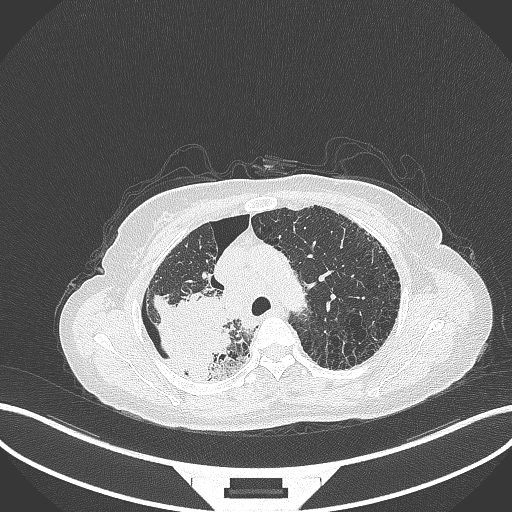
Chest CT, one axial slice. Reconstruction kernel B70f. 120 kVp. Lung window (W 1500 / L -600 HU). 512 × 512 image matrix, field of view 400 × 400 mm. Patient: female, 64 years. Case-level facts recorded for this patient, not image findings: clinical TNM (as recorded): T3 N3 M0.
Annotated regions visible in this slice (bounding box drawn by a radiologist):
- lung tumour (recorded histology: squamous cell carcinoma): bounding box [x1, y1, x2, y2] px = [150, 290, 235, 382]